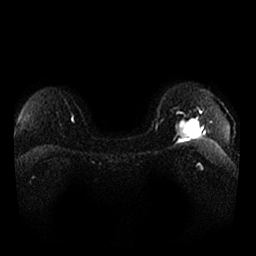
Breast MRI, one axial slice; slice 16 of 25 in the series (ordered by position); diffusion-weighted series; image 2 of 4 stored at this slice position (different b-values; order by instance number); 1.5 T; 4 mm slice thickness; 256 × 256 image matrix, field of view 340 × 340 mm. Female patient.
Structures marked on this image (expert manual segmentation):
- tumour on diffusion-weighted imaging: bounding box [x1, y1, x2, y2] px = [176, 118, 201, 139]